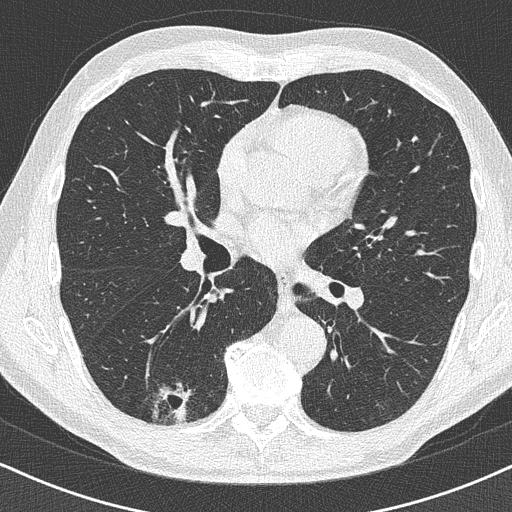
Axial slice from a low-dose chest CT screening exam. Baseline screening round. Lung window (W 1500 / L -600 HU). Lung (sharp) reconstruction kernel (B50f). Slice 210 of 438 in the series. 512 × 512 image matrix, field of view 320 × 320 mm. Male participant, aged 63 years at enrolment. Former smoker at enrolment.
• Lesion marked by an expert reader, bounding box (x1, y1, x2, y2) in pixels: (137, 371, 208, 430).
• Reader record for this screening exam (exam-level; its link to the box is not recorded): non-calcified nodule or mass ≥4 mm, right lower lobe, 16 × 13 mm, poorly defined margins.